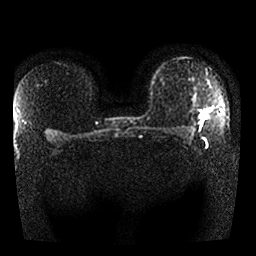
Breast MRI, one axial slice. Slice 19 of 25 in the series (ordered by position). Diffusion-weighted series; image 2 of 4 stored at this slice position (different b-values; order by instance number). 1.5 T. 4 mm slice thickness. 256 × 256 image matrix, field of view 340 × 340 mm. Female patient.
Structures marked on this image (outlined manually by an expert reader):
- tumour on diffusion-weighted imaging: bounding box <202,113,205,119> (left, top, right, bottom; pixels)